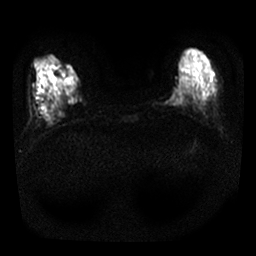
Breast MRI, one axial slice. Slice 7 of 24 in the series (ordered by position). Diffusion-weighted series; image 2 of 4 stored at this slice position (different b-values; order by instance number). 1.5 T. 256 × 256 image matrix. Female patient.
Annotated regions visible in this slice (manually delineated by an expert):
- tumour on diffusion-weighted imaging: bounding box <168,86,185,103> (left, top, right, bottom; pixels)